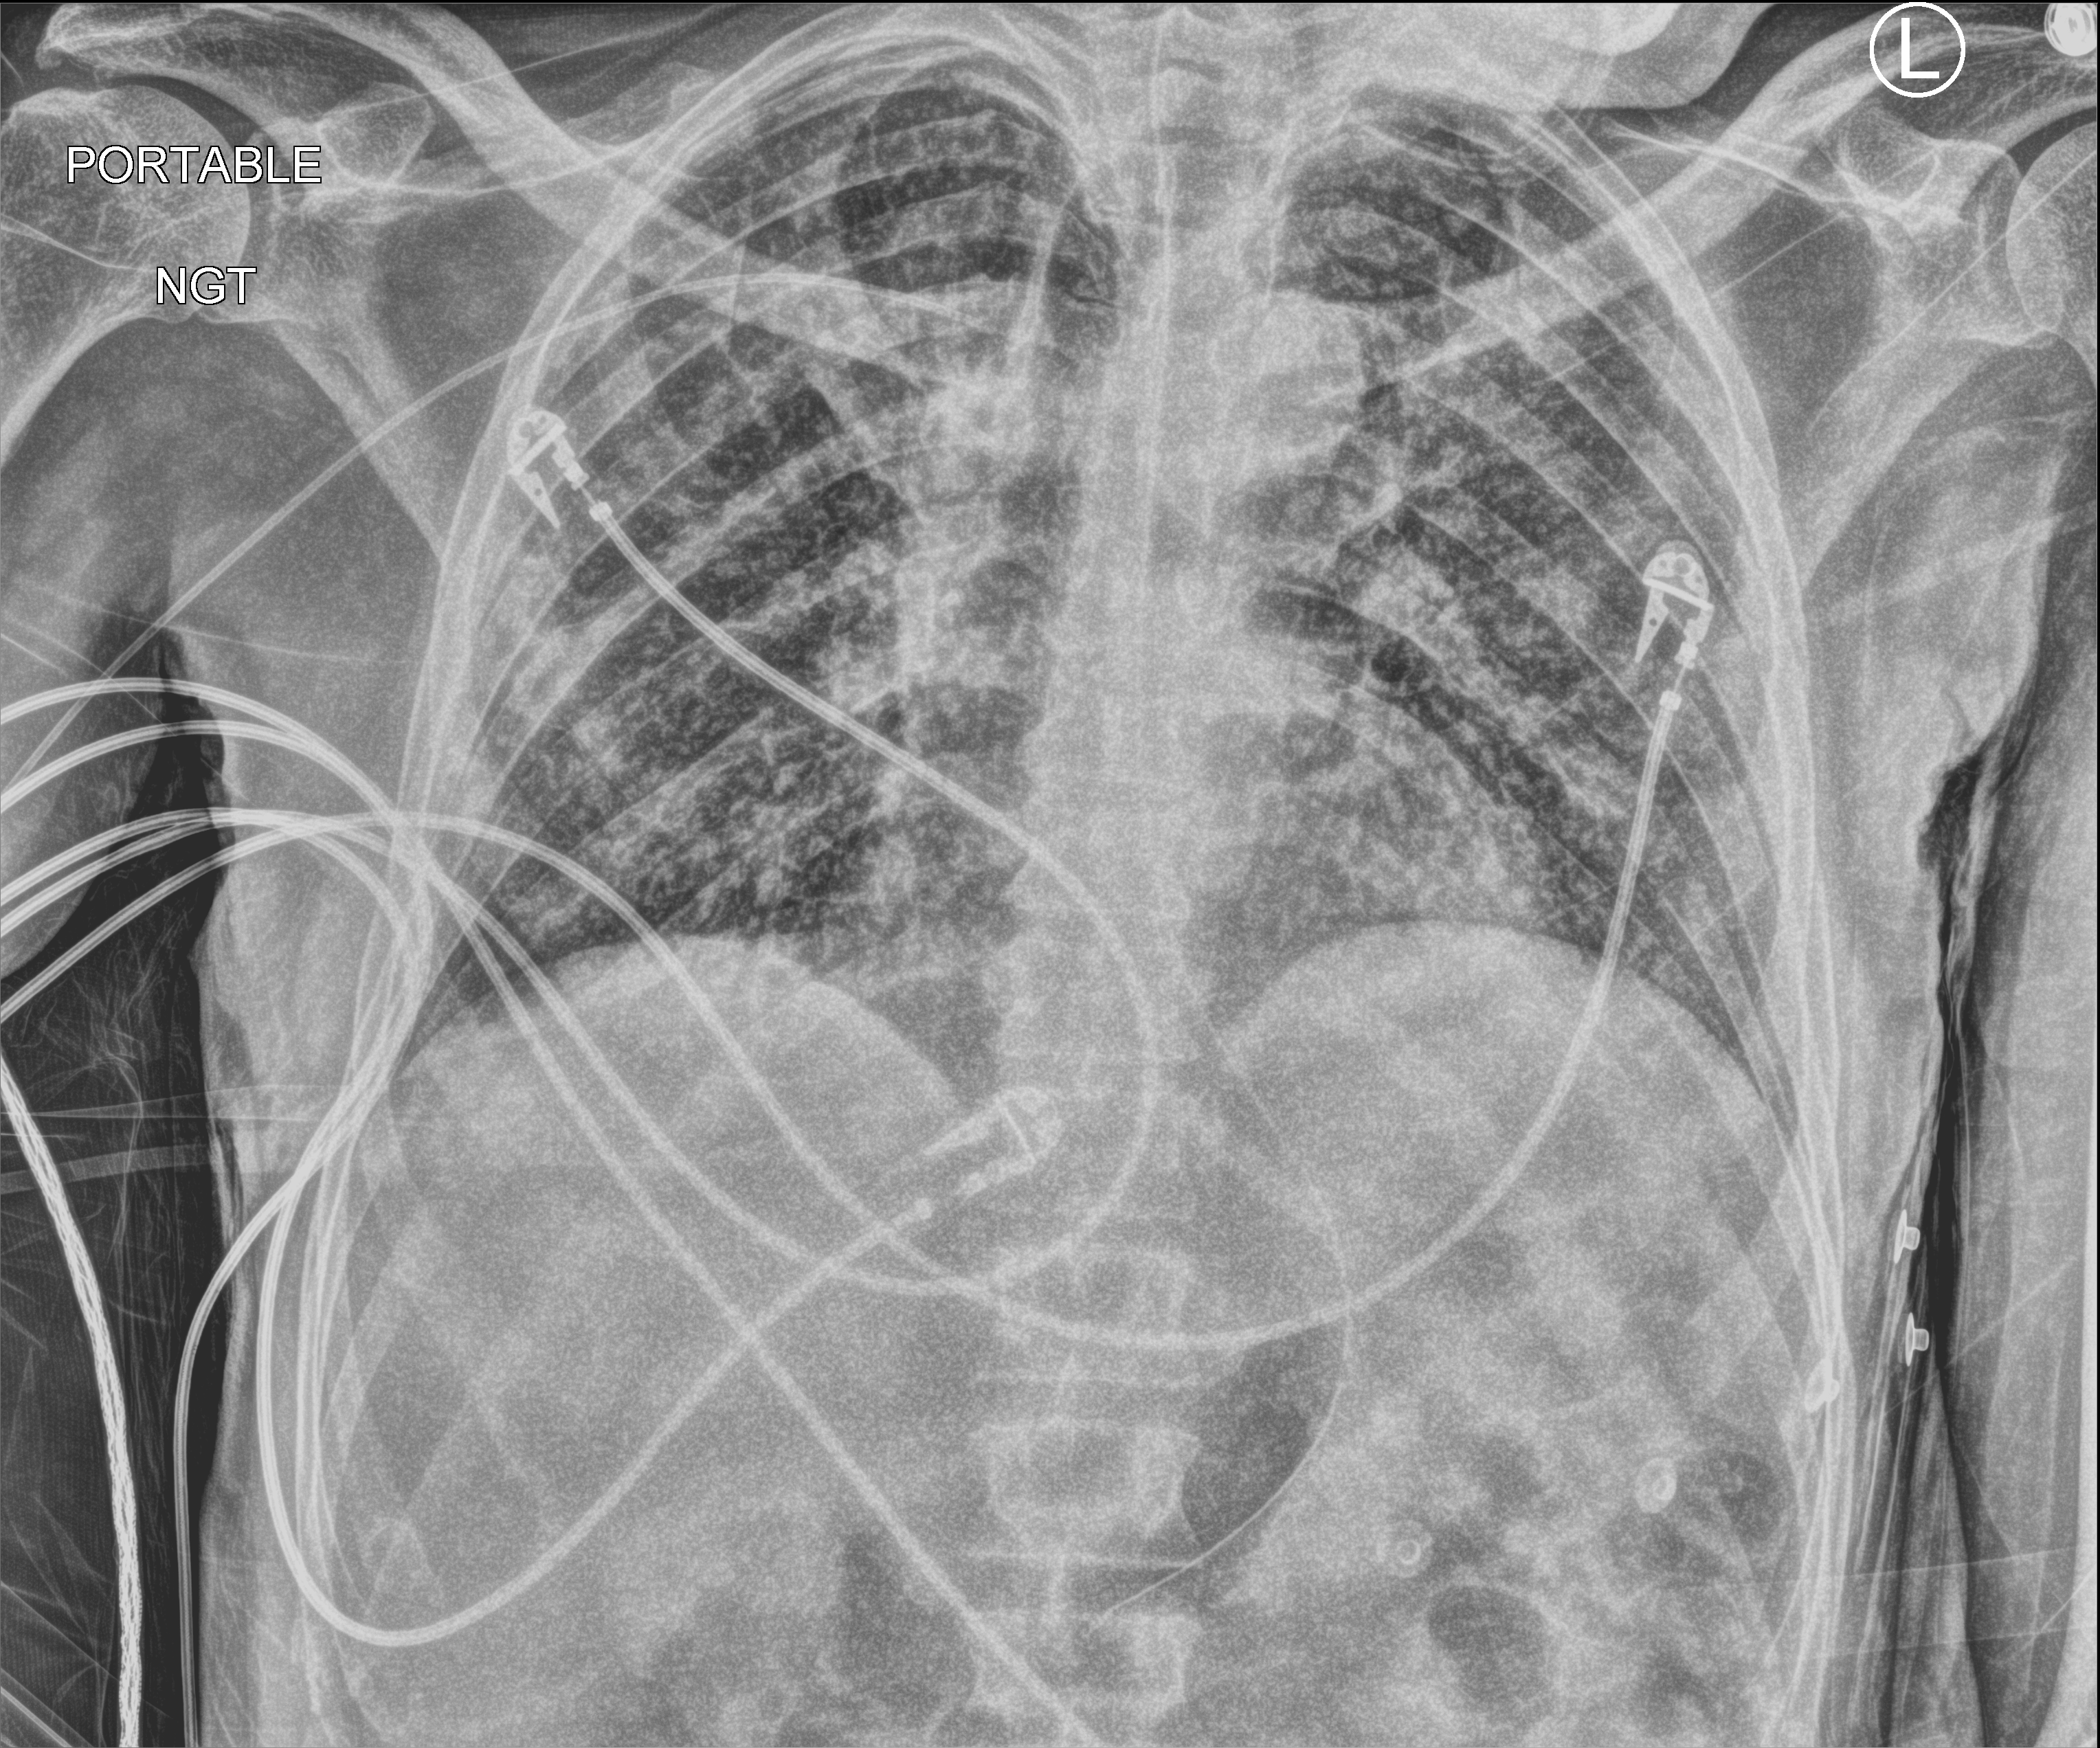
Bedside chest radiograph (computed radiography). Male patient hospitalised with COVID-19, age 18–59 years.
From the hospital-stay record, not from the radiograph (when in the stay this image was taken is not recorded):
- mechanically ventilated during this hospital stay: yes
- hypertension (admission record): no
- admitted to intensive care during this hospital stay: yes